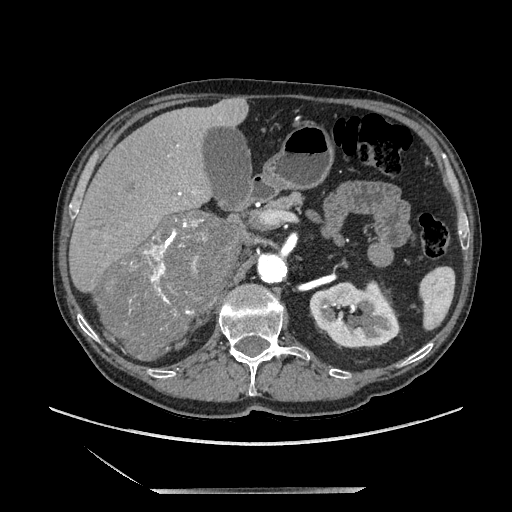
Contrast-enhanced abdominal CT, one axial slice. Slice 120 of 243 in the series (ordered by position). Soft-tissue window (W 400 / L 40 HU). 1.25 mm slice thickness. 512 × 512 image matrix, field of view 420 × 420 mm. Male patient. Case-level facts recorded for this patient, not image findings: diagnosis: adrenocortical carcinoma; tumour side: right adrenal; tumour size at pathology: 16 cm; Ki-67 index: 17 %; stage (as recorded): 3.
Structures marked on this image (semi-automatic segmentation, software-assisted and operator-edited):
- mass: box from (x=100, y=213) to (x=239, y=359) px